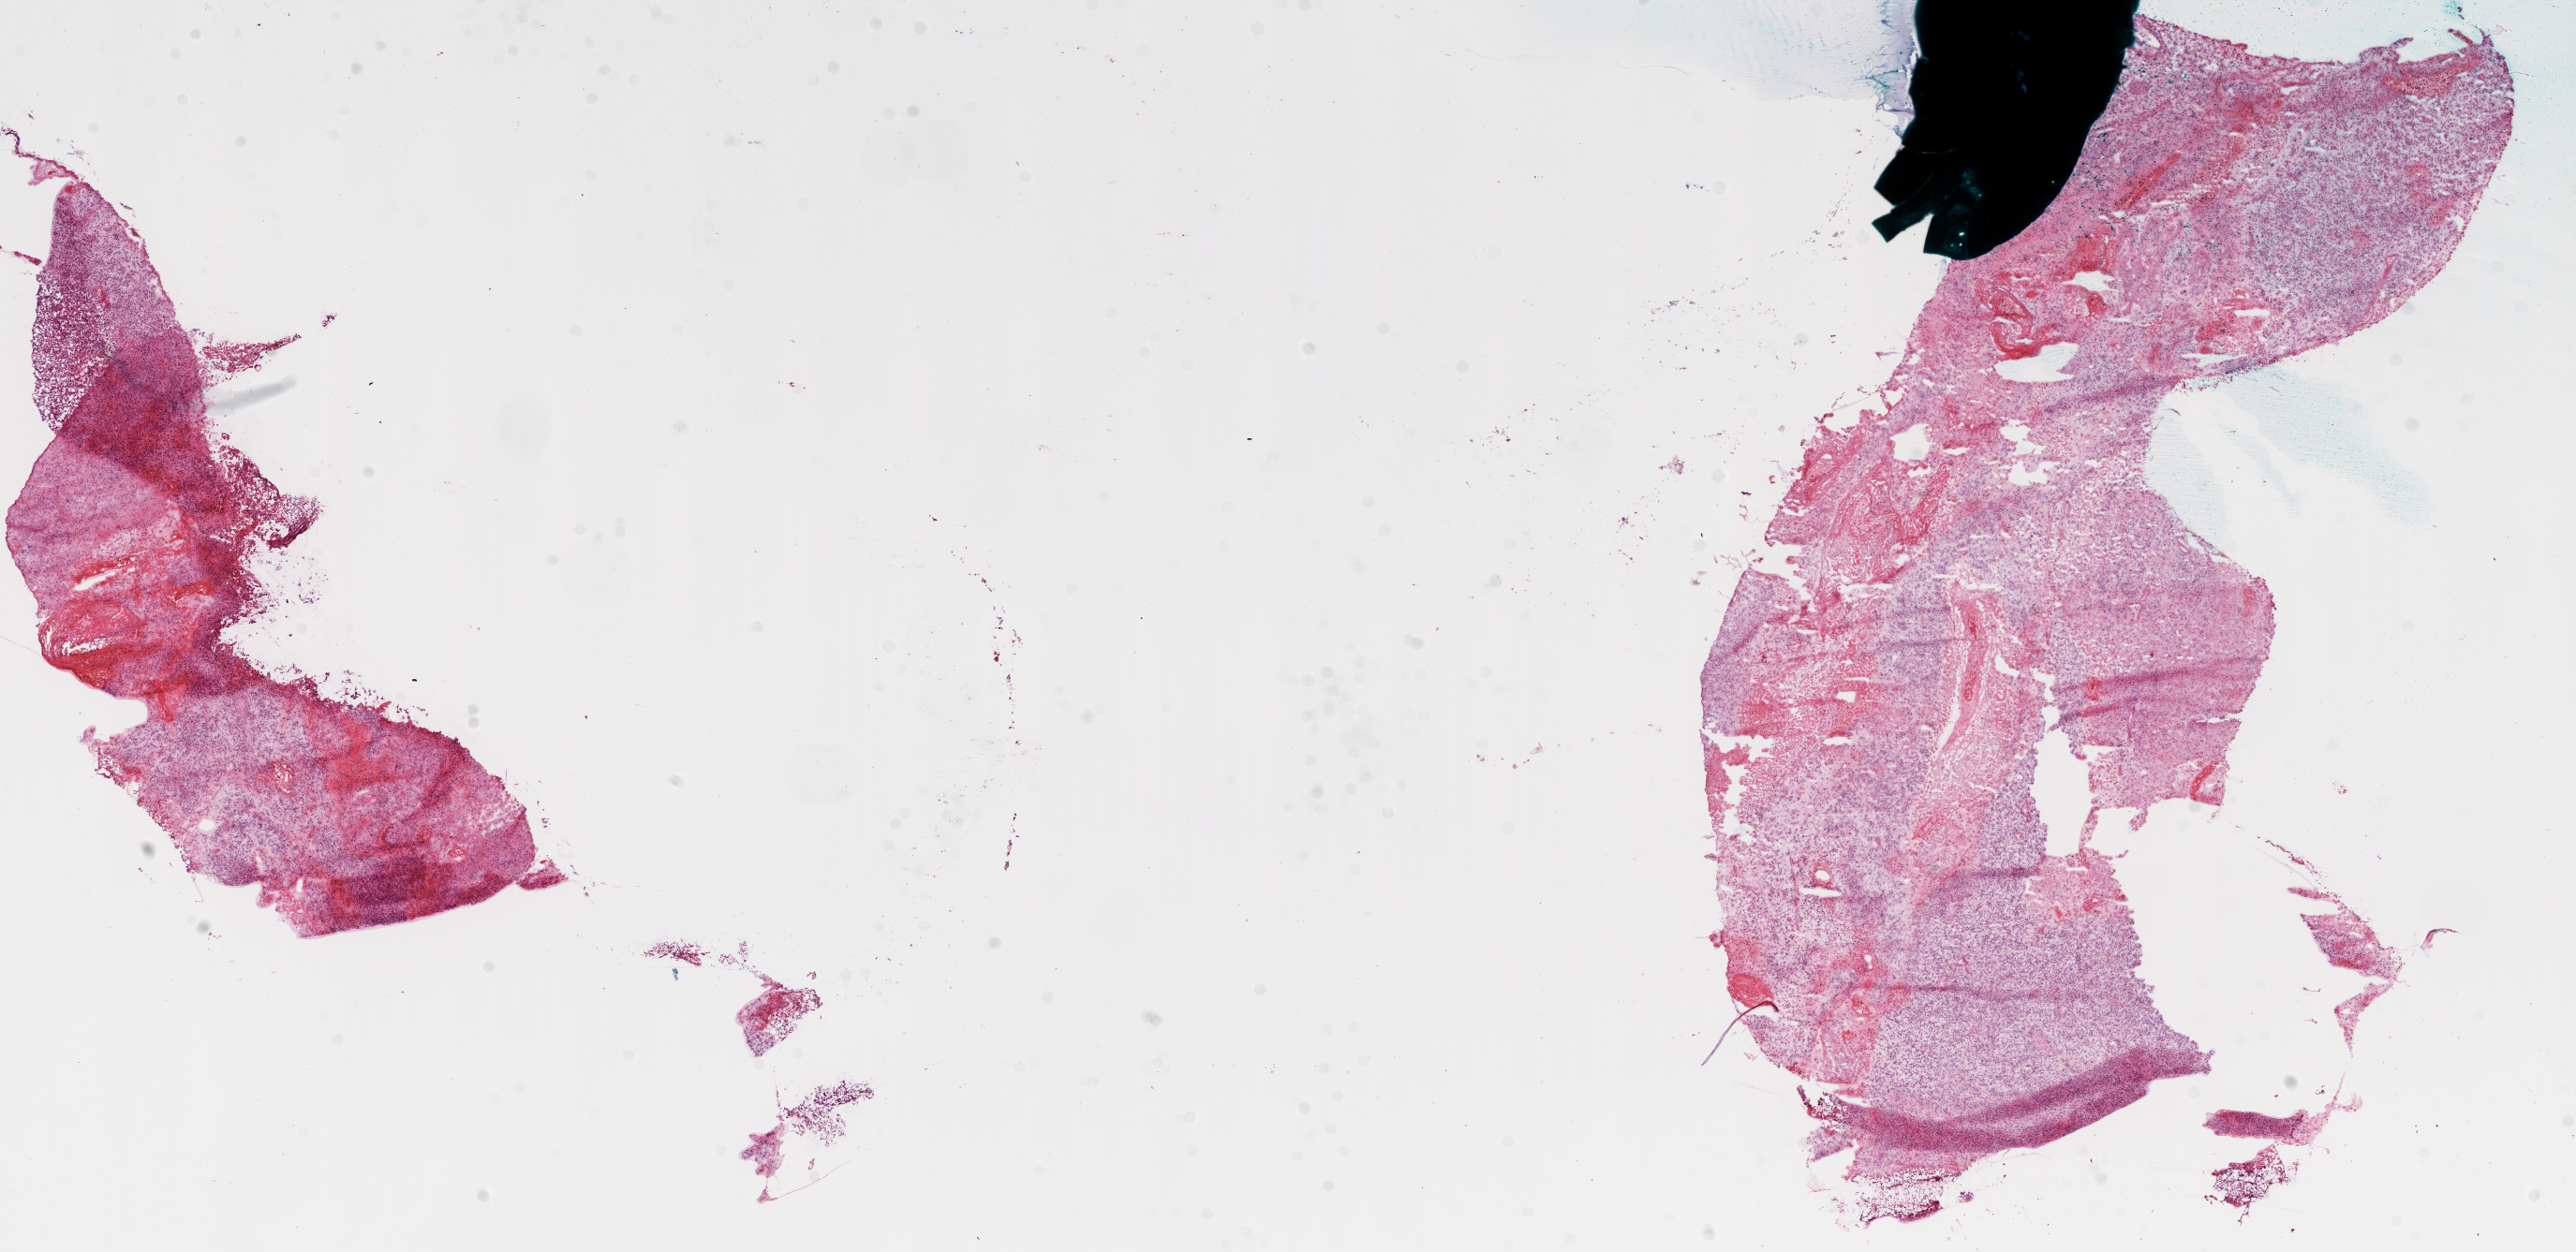
Whole-slide histology image, H&E-stained, low-resolution overview of the scanned area, about 22.1 x 10.7 mm; frozen section from the bottom of the tissue portion; brain, primary tumour sample. Female patient; age at initial diagnosis 54 years. Slide review estimates, as recorded: tumour cells 90%, tumour nuclei 100%, normal cells 0%, stromal cells 0%, necrosis 10%.
• pathologic diagnosis: Glioblastoma